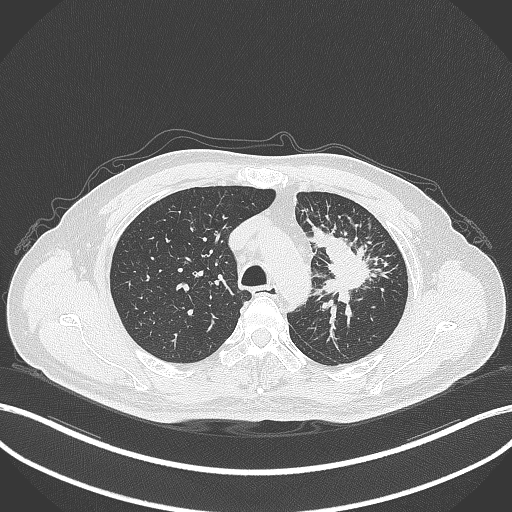
Chest CT, one axial slice. Position 268 of 386 along the scan axis. Reconstruction kernel B70f. Lung window (W 1500 / L -600 HU). 512 × 512 image matrix, field of view 400 × 400 mm. Male patient, age 69 years. Case-level facts recorded for this patient, not image findings: clinical TNM (as recorded): T2a N2 M0.
Outlined on this slice (bounding box drawn by a radiologist):
- lung tumour (recorded histology: adenocarcinoma): bounding box [x1, y1, x2, y2] px = [306, 219, 375, 303]